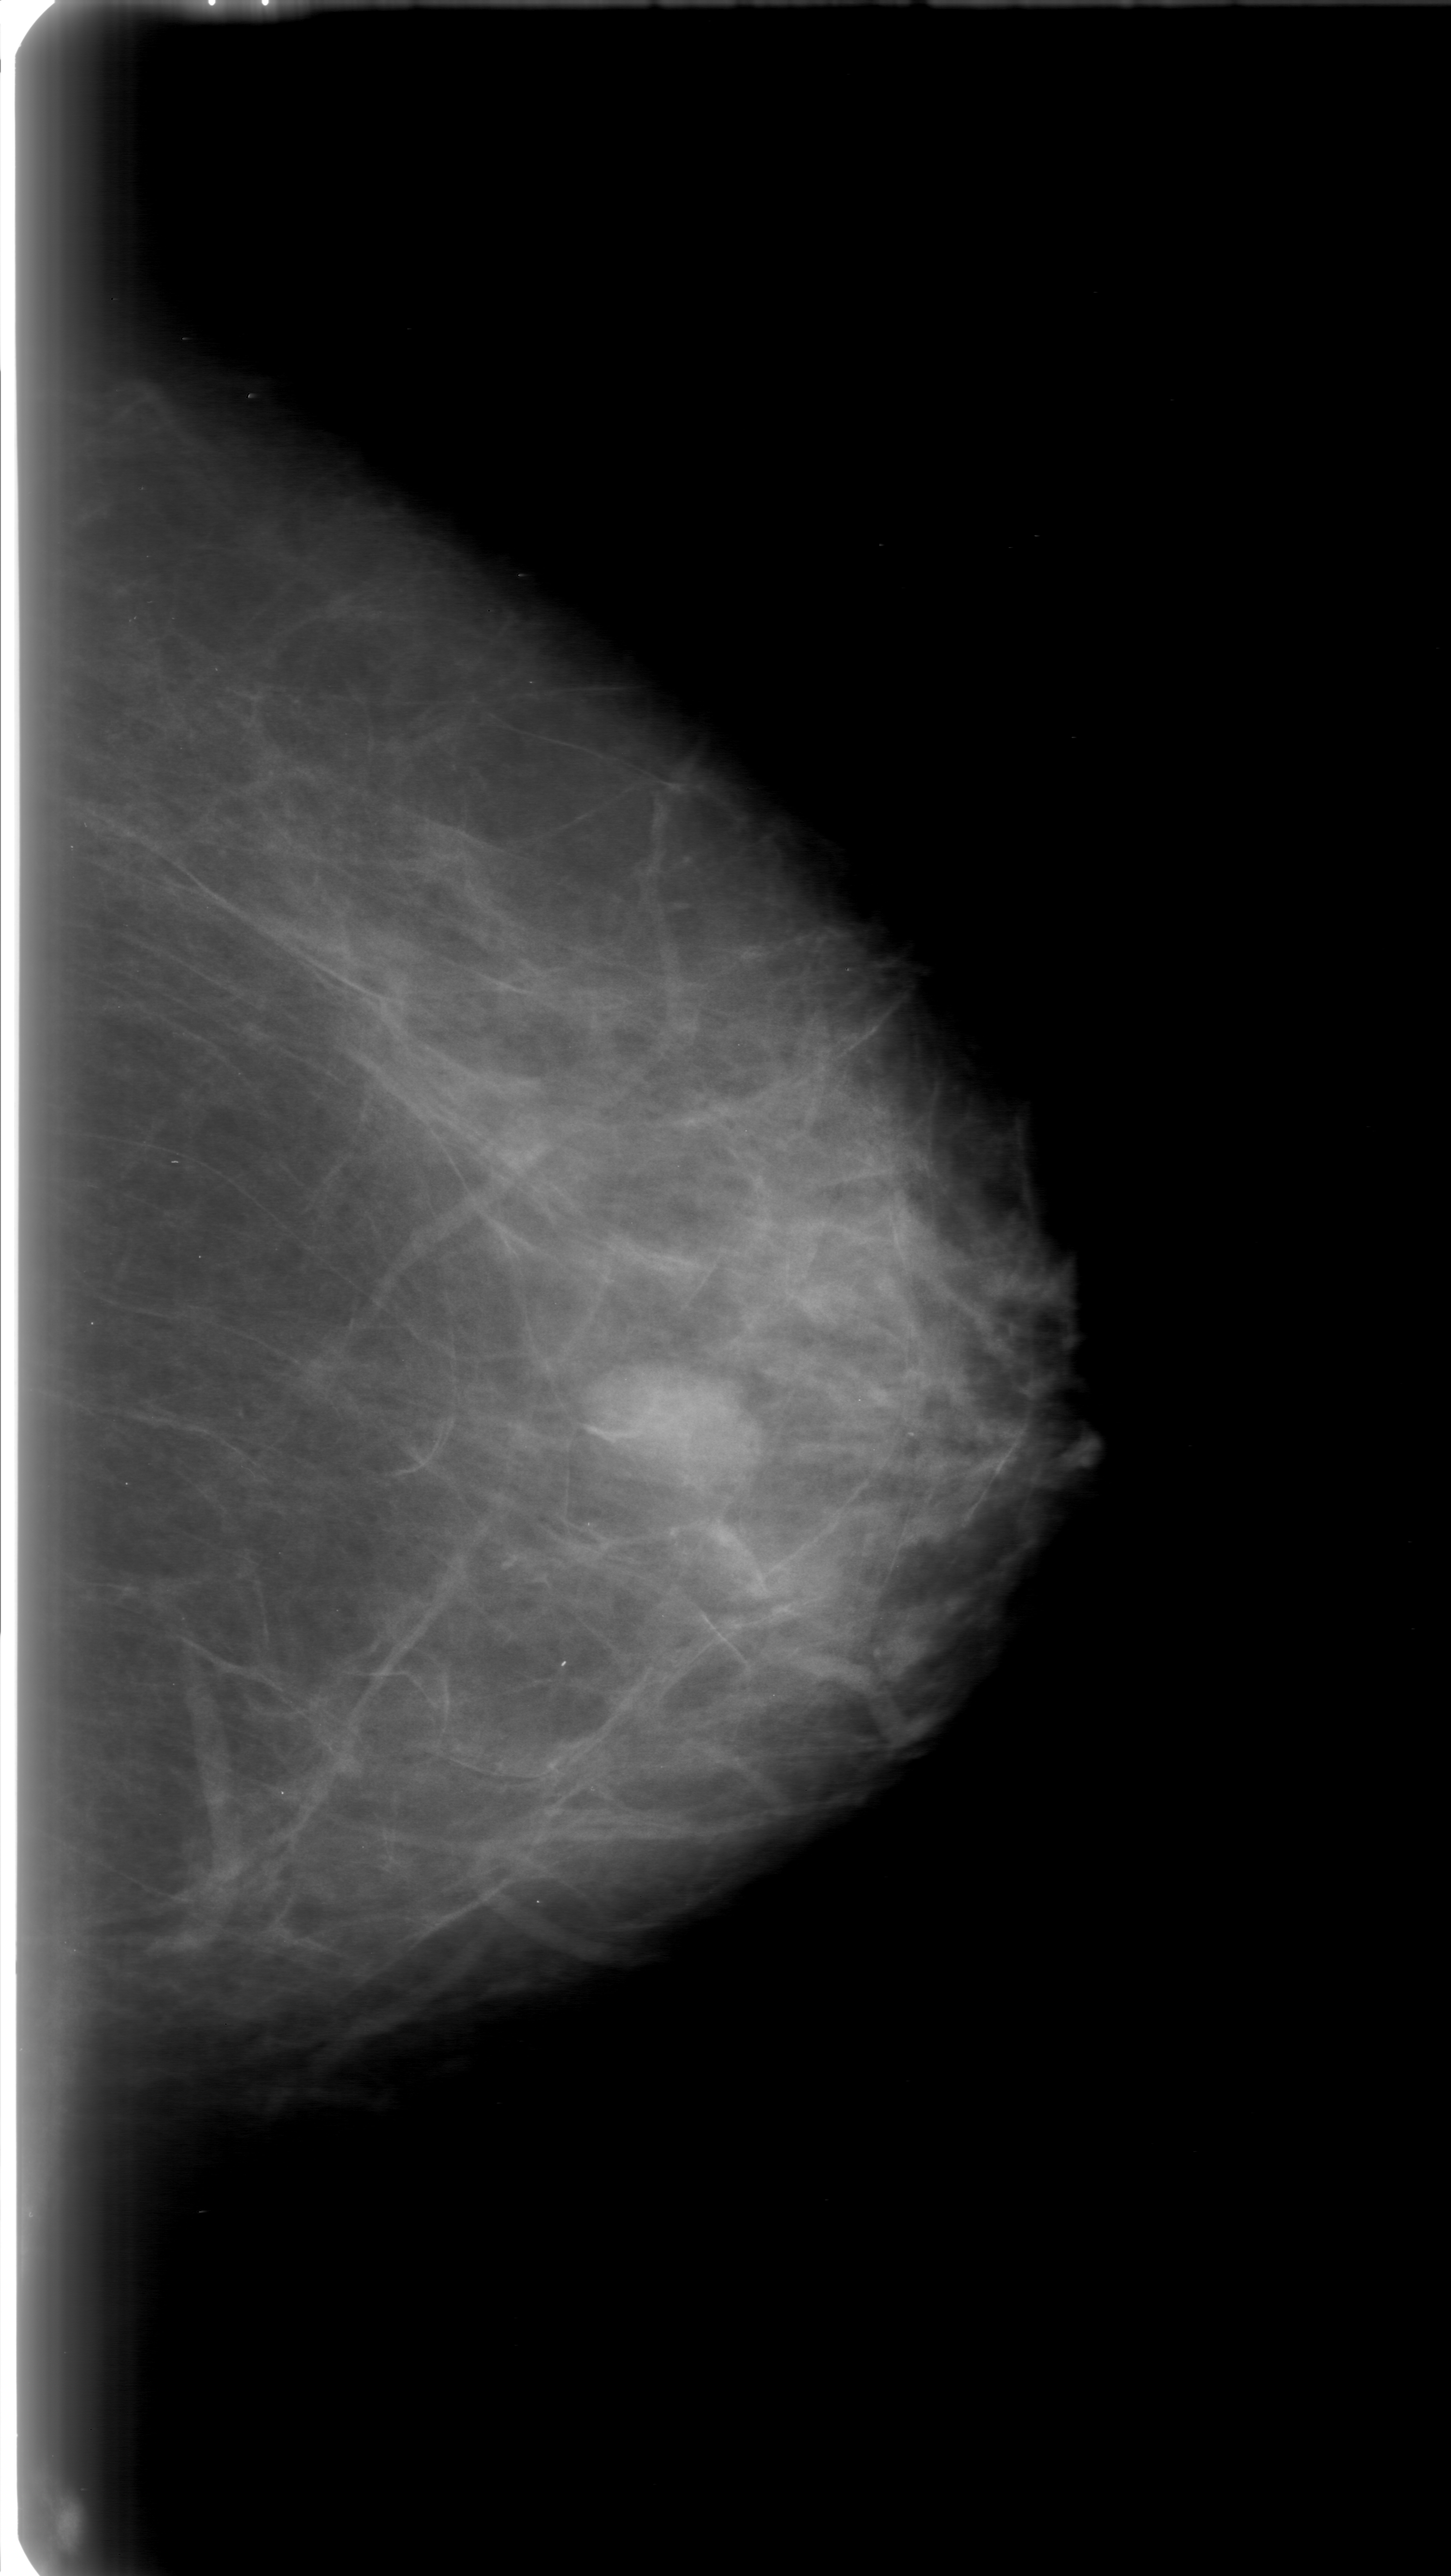
Mammogram (digitized film), left breast, craniocaudal (CC) view, BI-RADS breast density category 2 (scale 1–4).
Mass, shape oval, margins obscured; BI-RADS assessment category 0; subtlety rating 4 on a 1 (subtle) to 5 (obvious) scale; pathology (as recorded): benign.